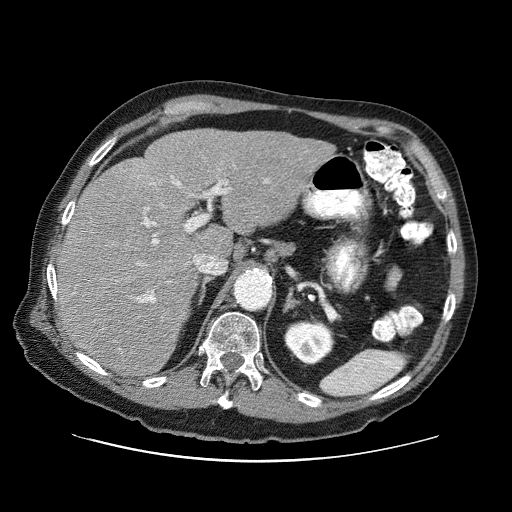
Contrast-enhanced abdominal CT (liver protocol), one axial slice; slice 47 of 87 in the series (ordered by position); reconstruction kernel STANDARD; 120 kVp; one of 3 acquisitions stored at this slice position; soft-tissue window (W 400 / L 40 HU); 2.5 mm slice thickness; 512 × 512 image matrix, field of view 400 × 400 mm. From the clinical record (not read from this slice): diagnosis: hepatocellular carcinoma (patient treated with transarterial chemoembolisation; whether this scan precedes or follows treatment is not stated here); TNM stage (as recorded): Stage-IIIA; Child-Pugh class: A; tumour differentiation: well differentiated.
Structures marked on this image (semi-automatically segmented with operator editing):
- liver parenchyma outside the tumour (the mass and vessels are separate outlines, so this box may not span the whole liver): bounding box [x1, y1, x2, y2] px = [56, 128, 334, 376]
- liver vessels: [74, 176, 268, 303]